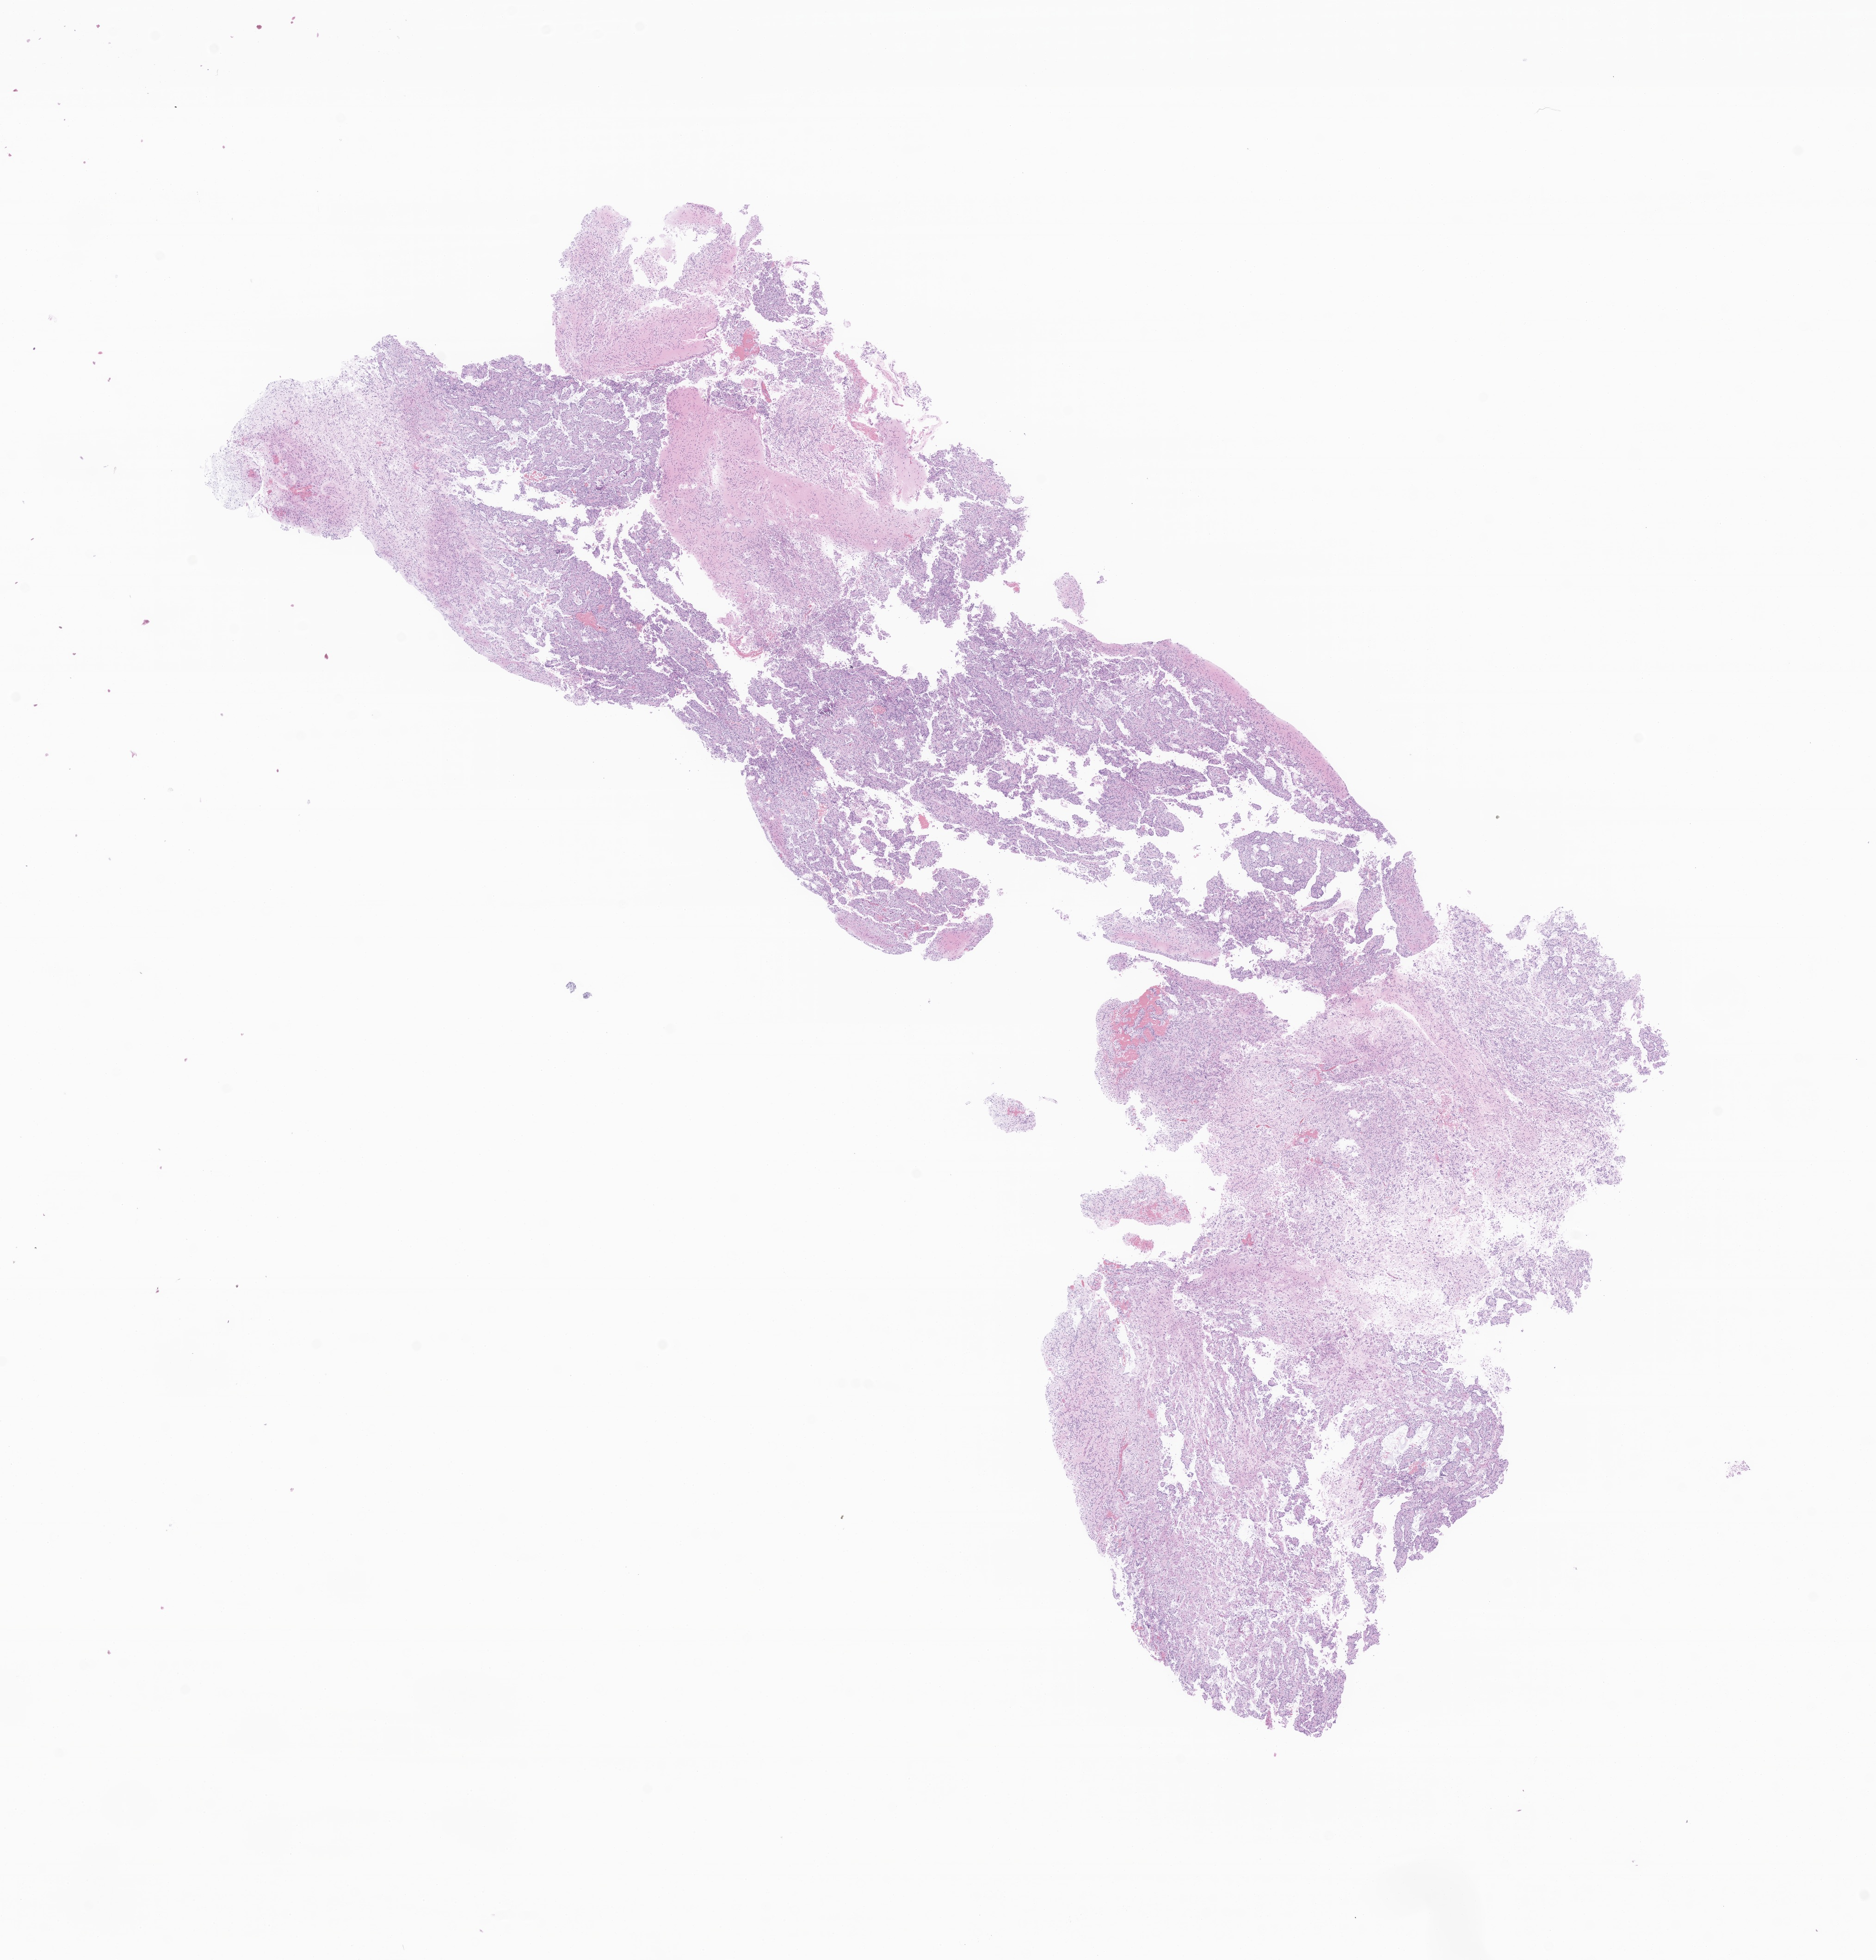
H&E whole-slide image of tumor tissue from the cerebellum, shown as a low-resolution overview of the whole scanned area (about 17.1 x 17.9 mm), FFPE section. Patient: female, age 229 months (19 years 1 month).
Diagnosis (ICD-O-3 morphology term): Glioma, malignant.